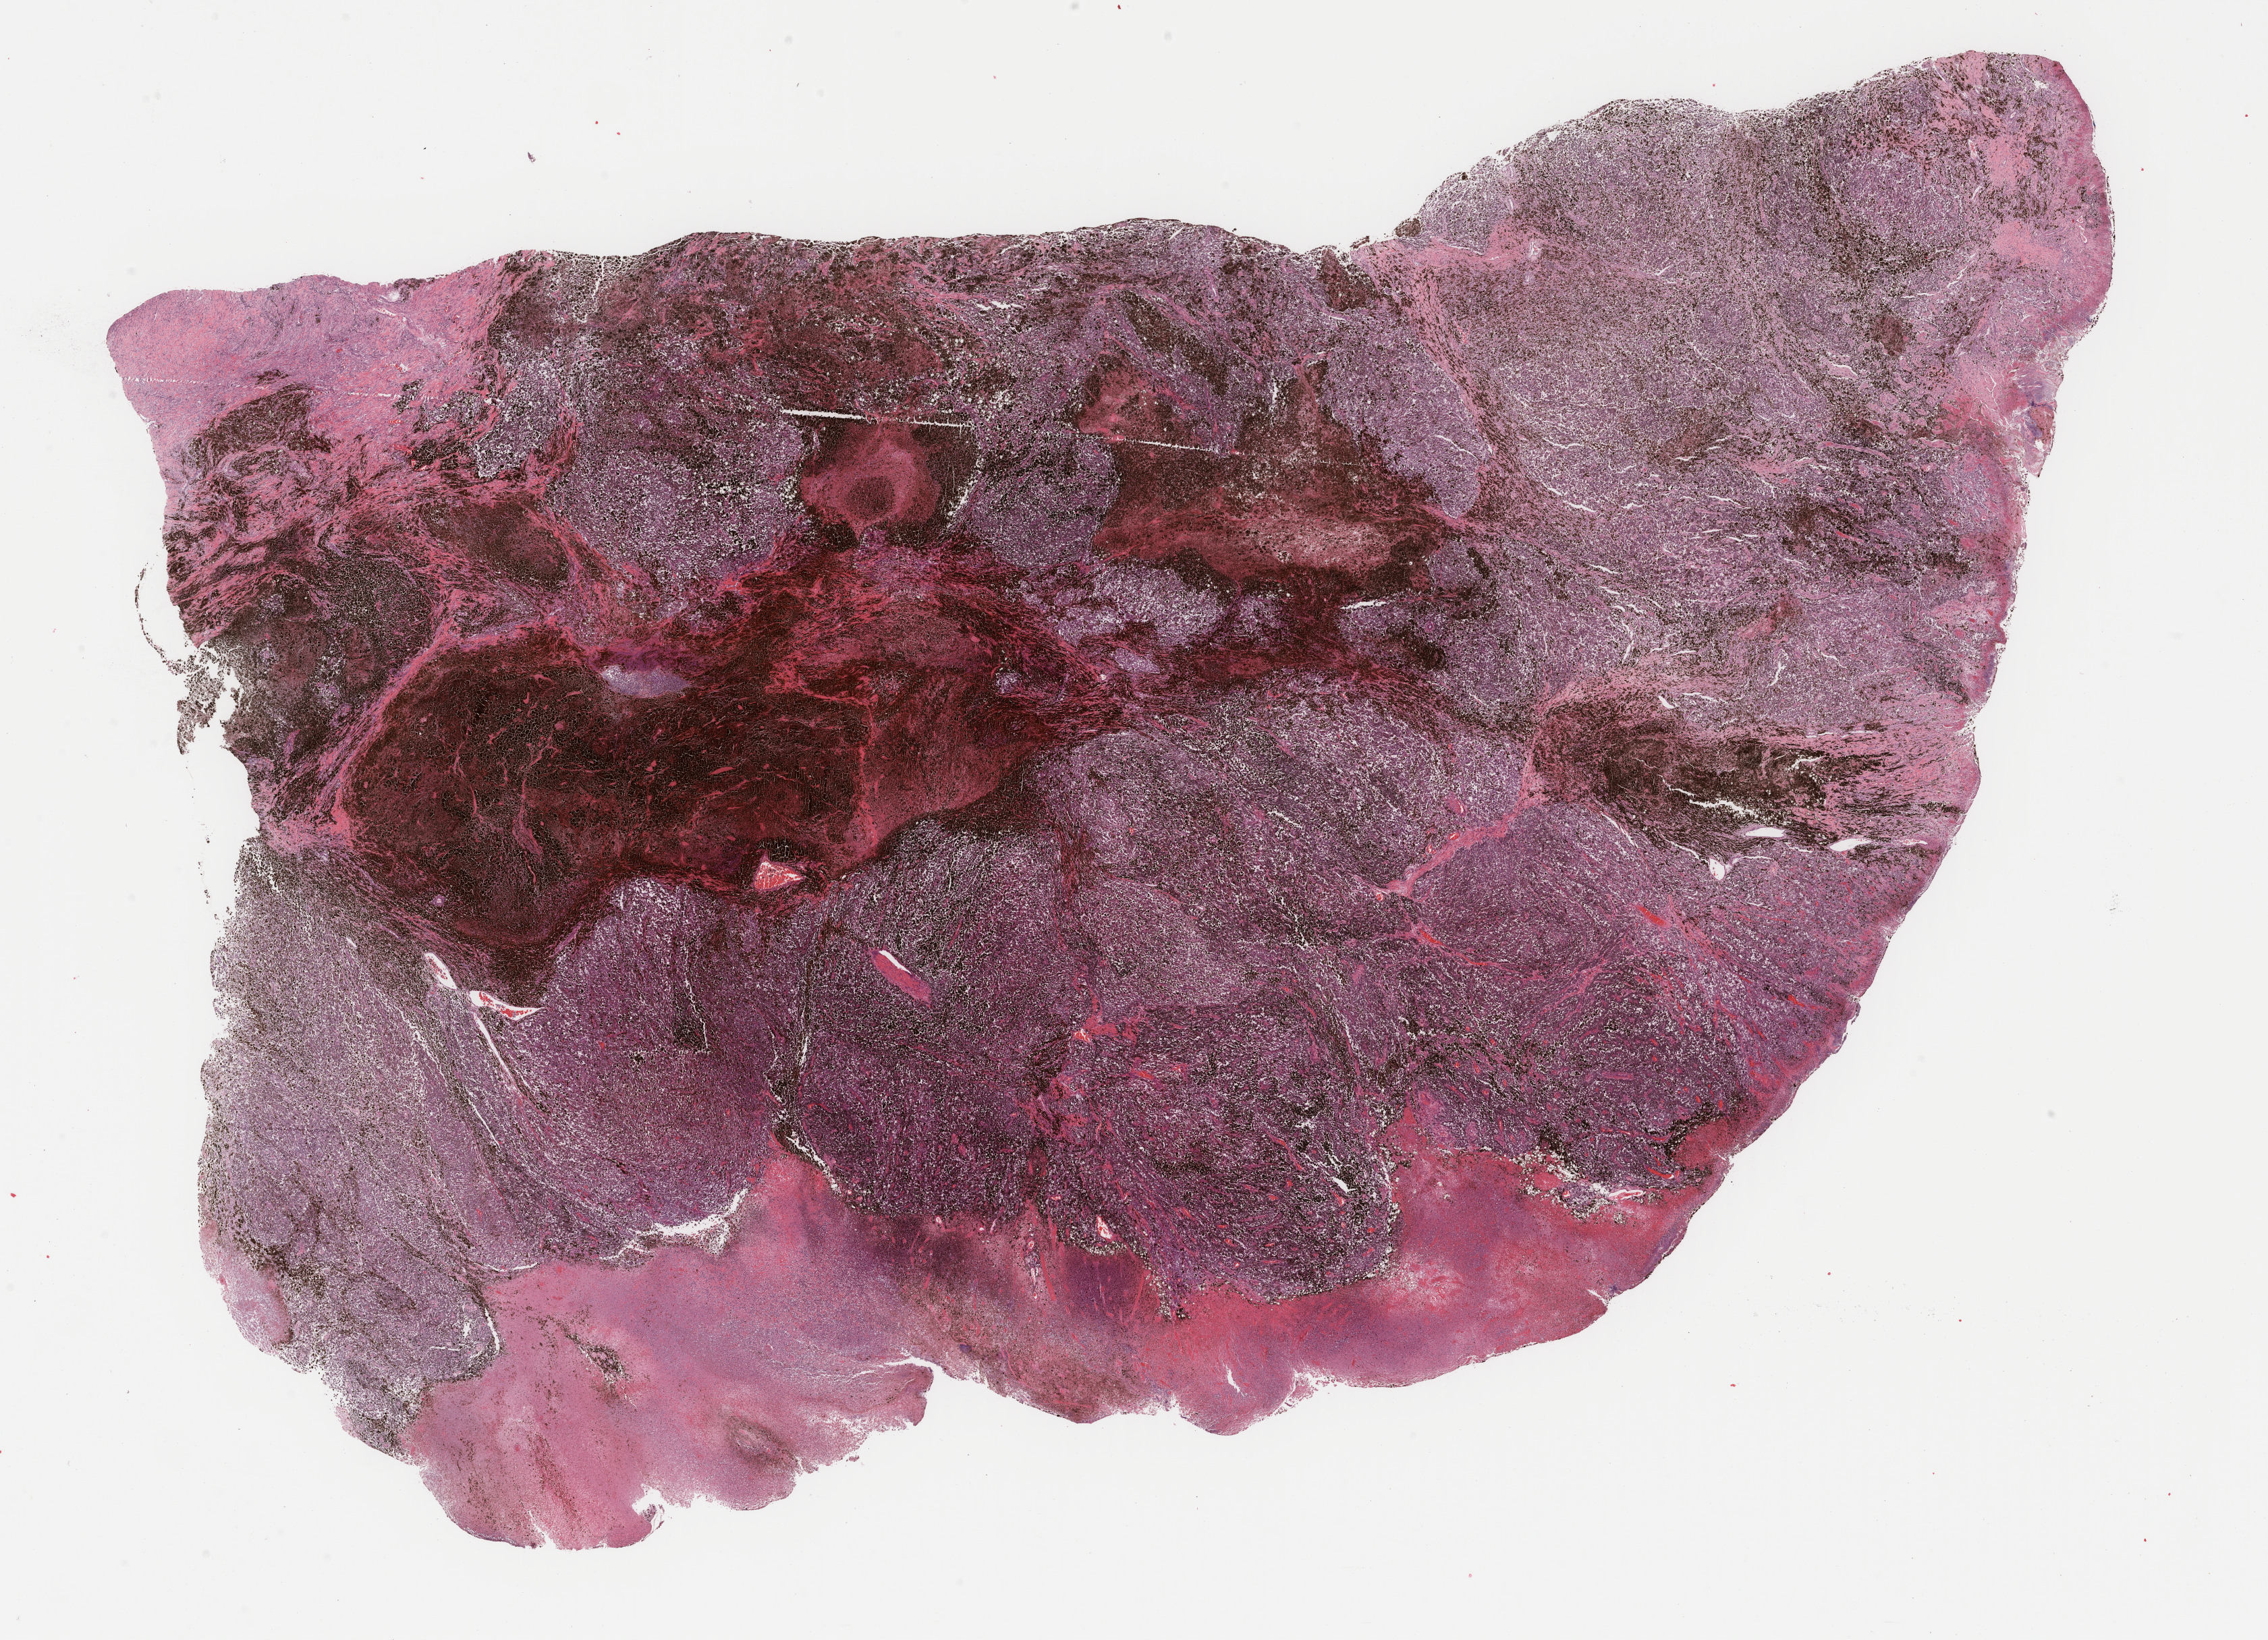
Digitized Hematoxylin and eosin (H&E) stained tissue section (whole slide), shown as a low-resolution overview of the whole scanned area (about 26.7 x 19.3 mm, slide scanned at 40x); formalin-fixed paraffin-embedded (FFPE) diagnostic section; skin, primary tumour sample. Patient sex: female.
Pathologic diagnosis: Malignant melanoma, NOS.